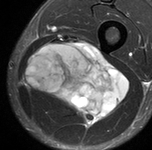
MRI of an extremity soft-tissue mass, one axial slice. Slice 44 of 90 in the series (ordered by position). STIR. MR volume resampled by the dataset authors to the PET/CT grid (not the native acquisition matrix). 3.27 mm slice thickness. 152 × 150 image matrix, field of view 148 × 146 mm. Male patient. From the clinical record (not read from this slice): histological type: undifferentiated pleomorphic liposarcoma; grade: high; site of the primary tumour: left thigh.
Outlined on this slice (expert contour drawn on MRI and transferred to this co-registered scan by the dataset authors):
- gross tumour volume including surrounding oedema: box from (x=25, y=43) to (x=129, y=124) px
- gross tumour volume (mass): (x=25, y=43)–(x=129, y=124)